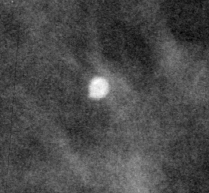
Crop from a digitized film mammogram around one marked abnormality; left breast; MLO view.
Finding: calcifications, morphology lucent center; BI-RADS assessment category 2; subtlety rating 5 on a 1 (subtle) to 5 (obvious) scale; benign; no additional work-up was recommended (benign without callback).